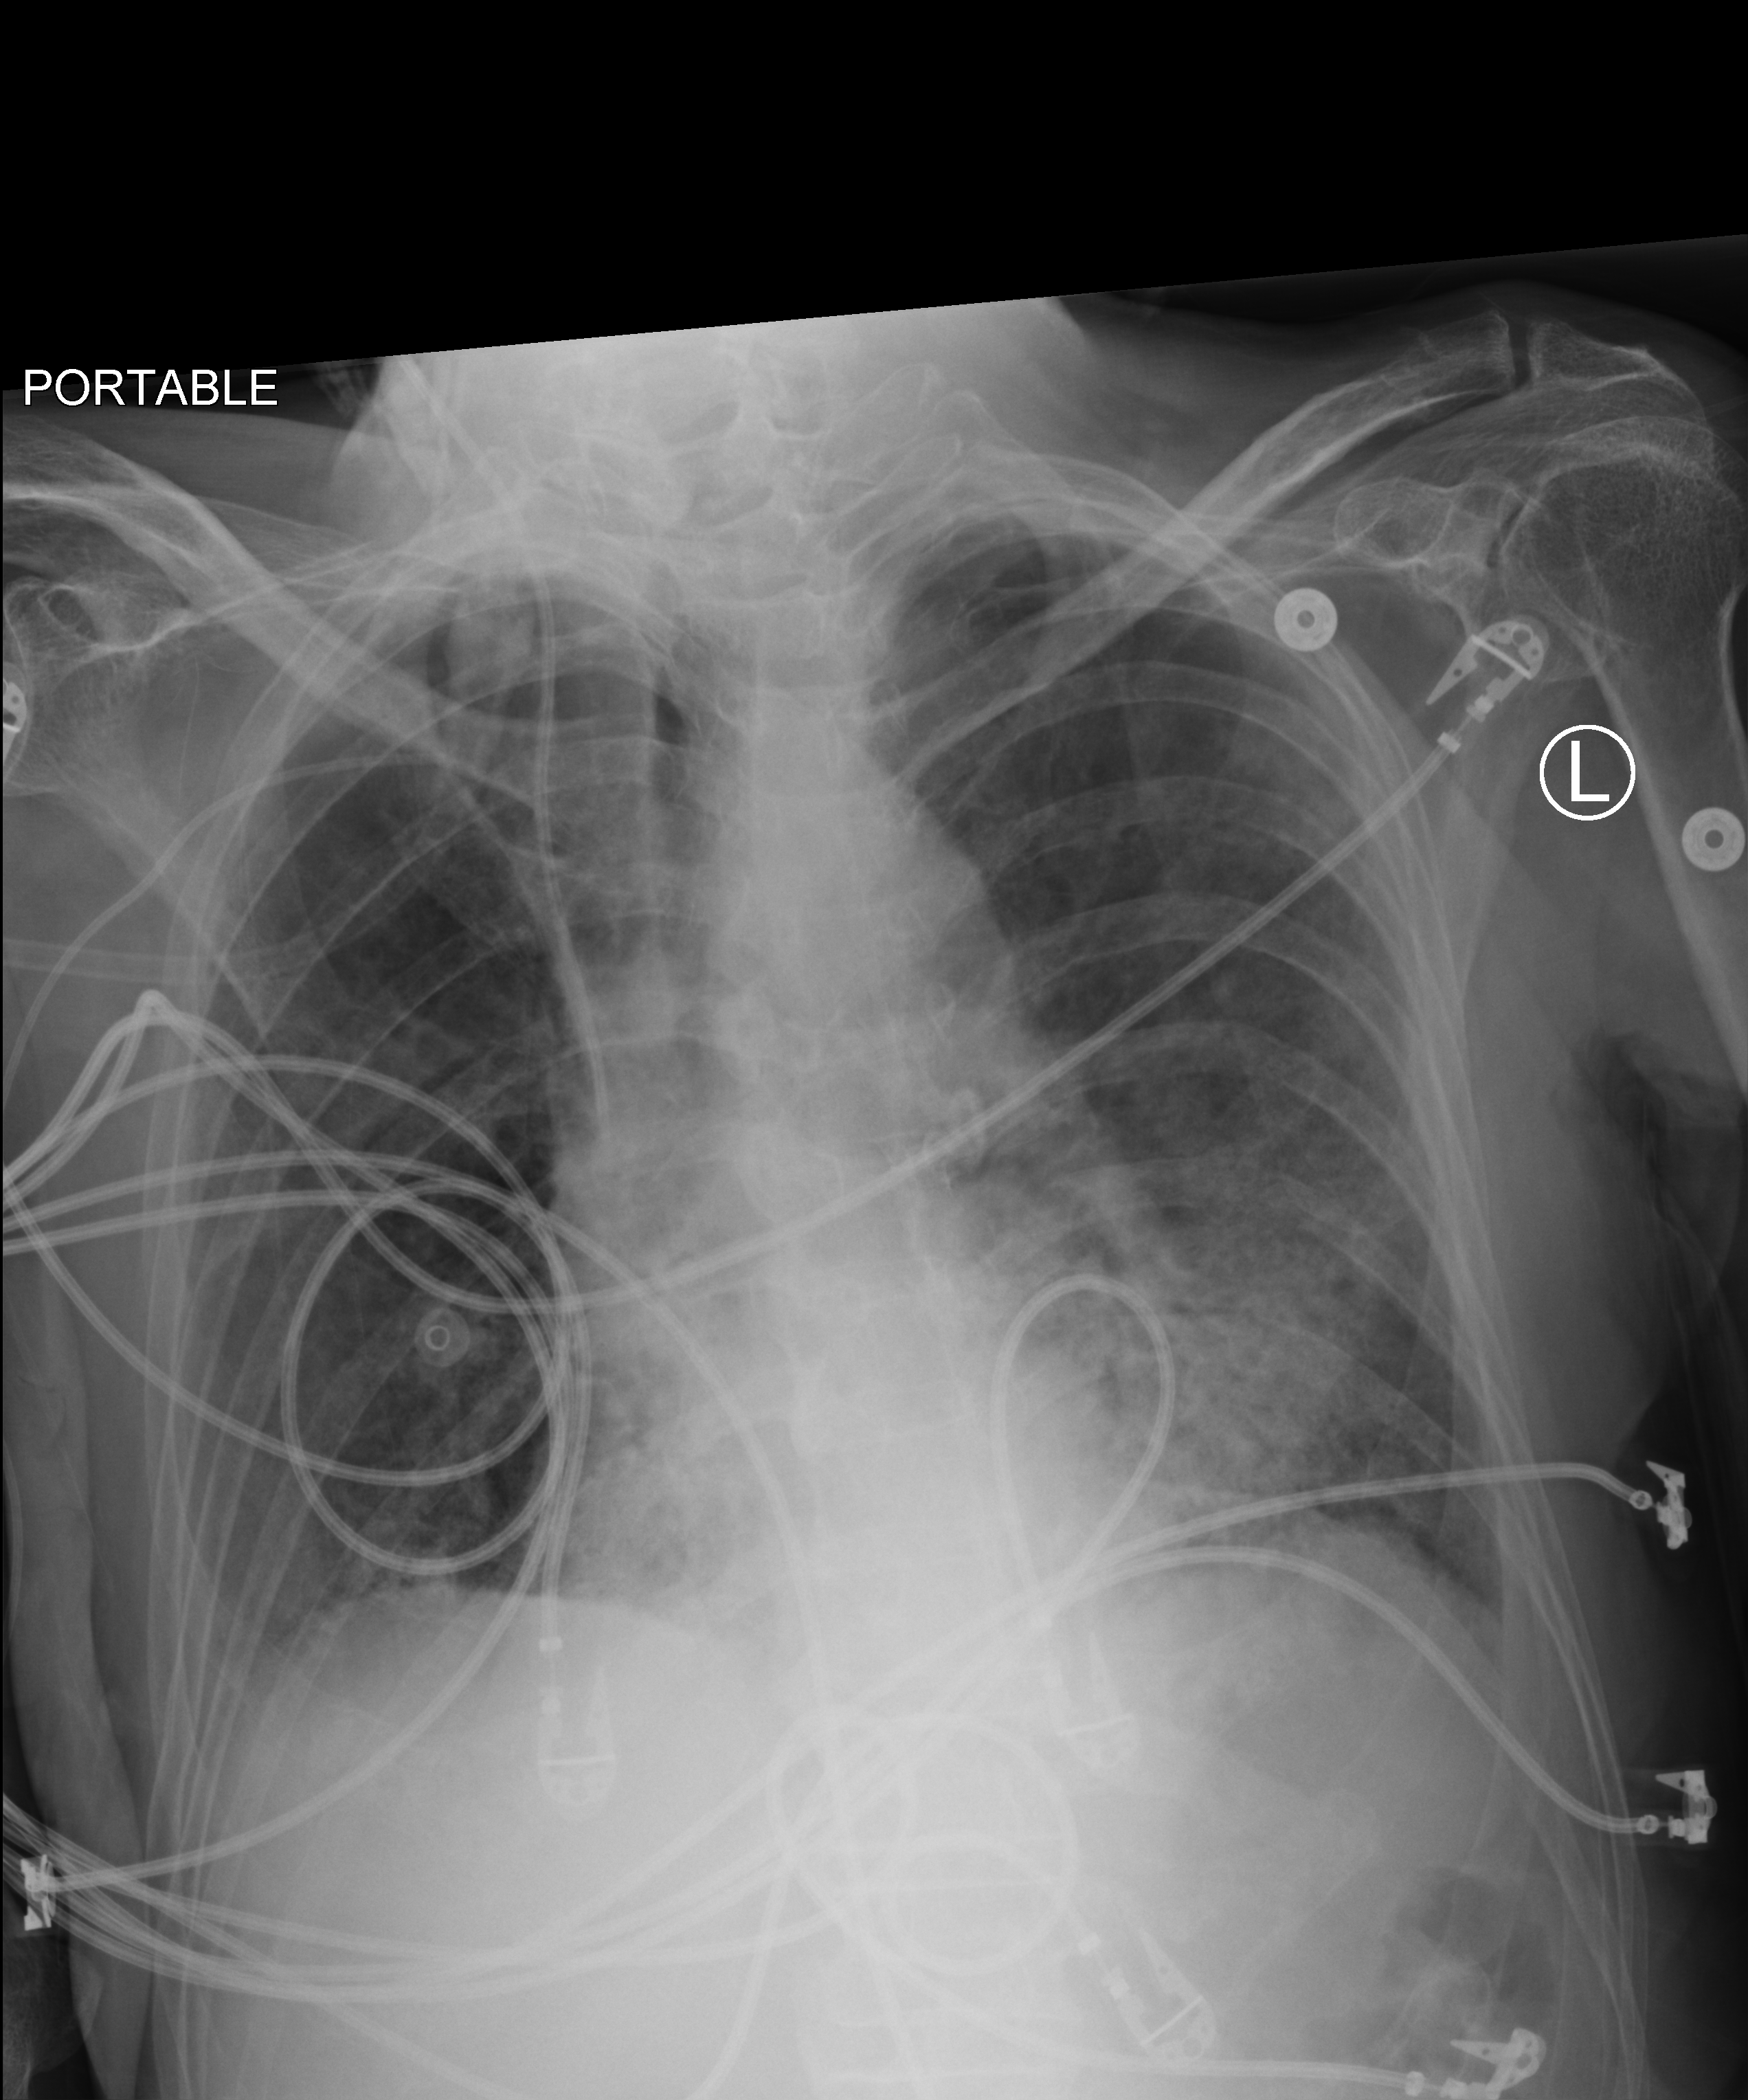
Bedside chest radiograph (computed radiography), anteroposterior (AP) projection. Male patient hospitalised with COVID-19, age 60–74 years.
Admission-level facts for this patient (not findings on this image; timing relative to this image not recorded): hypertension (admission record): yes.